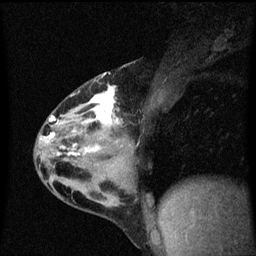
Breast MRI (dynamic contrast-enhanced), one sagittal slice; slice 33 of 60 in the series (ordered by position); dynamic contrast-enhanced series, image 2 of 3 at this slice position (ordered by acquisition); 1.5 T; TE 4.2 ms, TR 8.4 ms; 2 mm slice thickness; 256 × 256 image matrix. Patient: female, 32 years.
Annotated regions visible in this slice (semi-automatic segmentation, software-assisted and operator-edited):
- analysis volume of interest (the breast-tissue region the enhancement analysis was run in; not a lesion): bounding box <35,74,151,169> (left, top, right, bottom; pixels)
- tumour enhancement mask (voxels above the 70 % enhancement threshold inside the analysis volume of interest): <48,74,122,157>